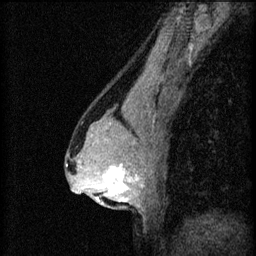
Breast MRI (dynamic contrast-enhanced), one sagittal slice; slice 37 of 60 in the series (ordered by position); 3 images stored at this slice position (order not interpretable as contrast timing); 1.5 T; TE 4.2 ms, TR 8.2 ms; 2 mm slice thickness; 256 × 256 image matrix, field of view 180 × 180 mm. Female patient, age 44 years.
Outlined on this slice (semi-automatic segmentation, software-assisted and operator-edited):
- analysis volume of interest (the breast-tissue region the enhancement analysis was run in; not a lesion): bounding box <94,162,143,205> (left, top, right, bottom; pixels)
- tumour enhancement mask (voxels above the 70 % enhancement threshold inside the analysis volume of interest): <96,164,139,203>